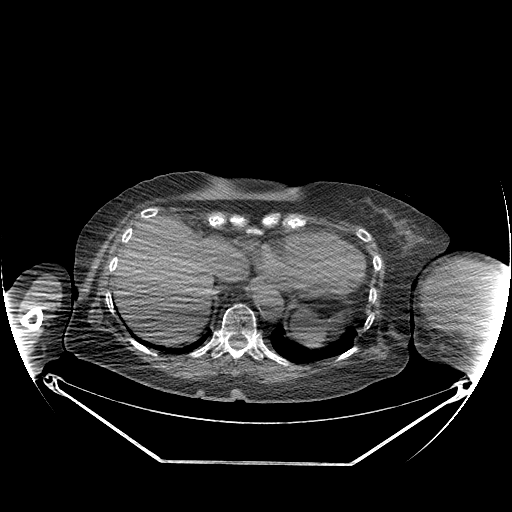
CT of an extremity soft-tissue mass (from a PET/CT study), one axial slice; slice 144 of 267 in the series (ordered by position); reconstruction kernel STANDARD; soft-tissue window (W 400 / L 40 HU); 512 × 512 image matrix, field of view 500 × 500 mm. Female patient. From the clinical record (not read from this slice): histological type: pleiomorphic leiomyosarcoma; grade: high; site of the primary tumour: left biceps.
Outlined on this slice (expert contour drawn on MRI and transferred to this co-registered scan by the dataset authors):
- gross tumour volume including surrounding oedema: bounding box [x1, y1, x2, y2] px = [429, 263, 499, 321]
- gross tumour volume (mass): [429, 263, 497, 314]